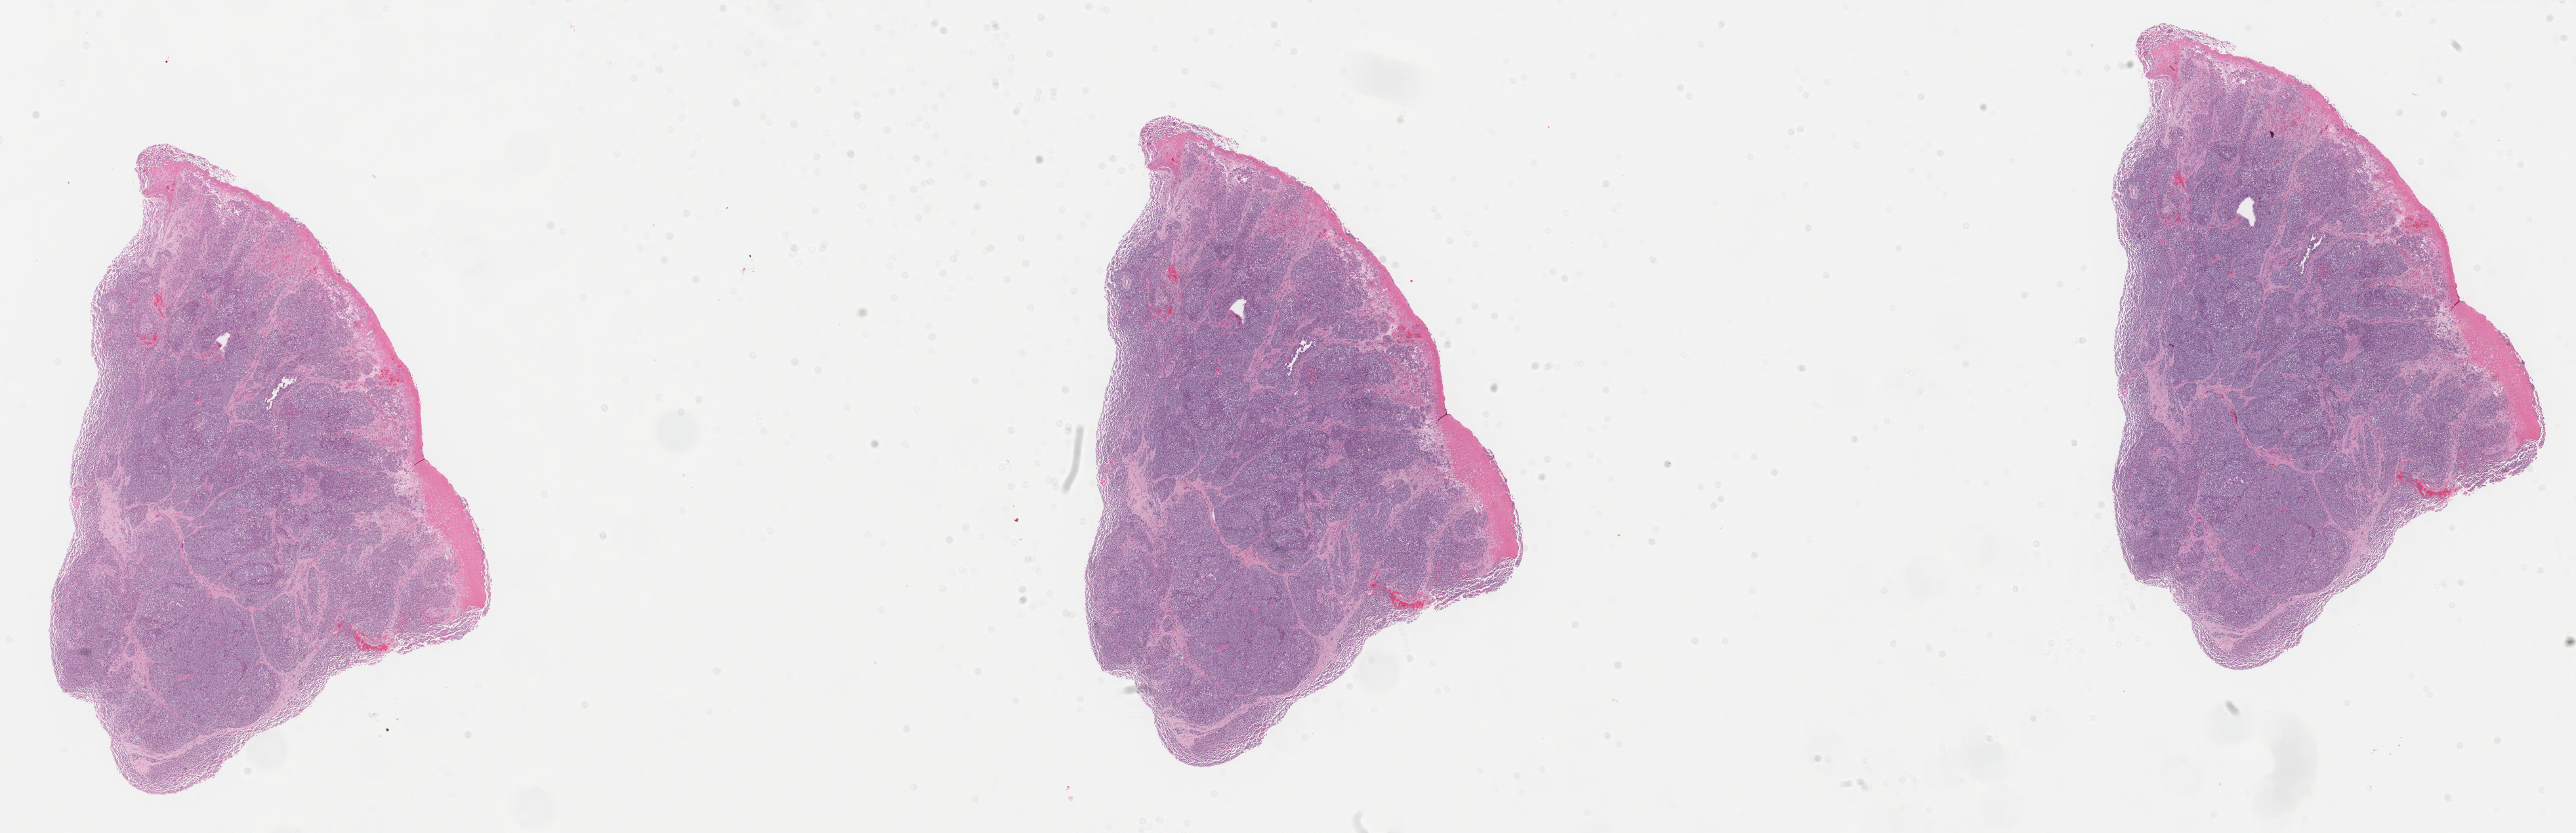
H&E-stained whole-slide image, whole scanned area (about 31.1 x 10.0 mm, from a 40x scan) shown as a low-resolution overview; formalin-fixed paraffin-embedded (FFPE) diagnostic section; primary tumour sample from the skin. Patient: female, age at initial diagnosis 49 years.
* AJCC pathologic stage: IIC (6th edition)
* histologic diagnosis: Malignant melanoma, NOS
* TNM: T4b N0 M0